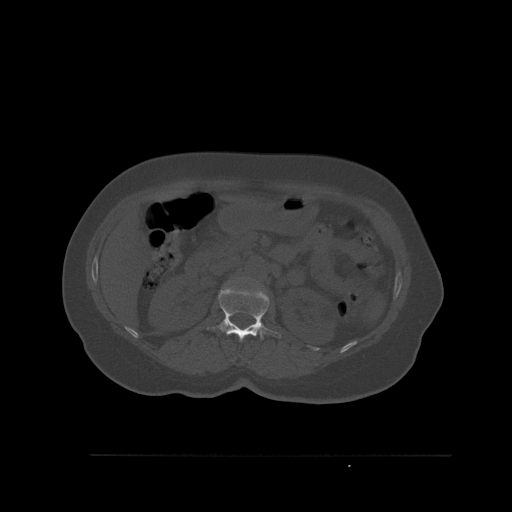
CT including the spine, one axial slice; slice 264 of 527 in the series (ordered by position); bone window (W 1800 / L 400 HU); 1.5 mm slice thickness; 512 × 512 image matrix, field of view 470 × 470 mm. Patient: female, 73 years. Case-level facts recorded for this patient, not image findings: primary cancer: breast.
Annotated regions visible in this slice (semi-automatic segmentation, software-assisted and operator-edited):
- L1 vertebra: bounding box (x1, y1, x2, y2) in pixels: (207, 285, 281, 341)